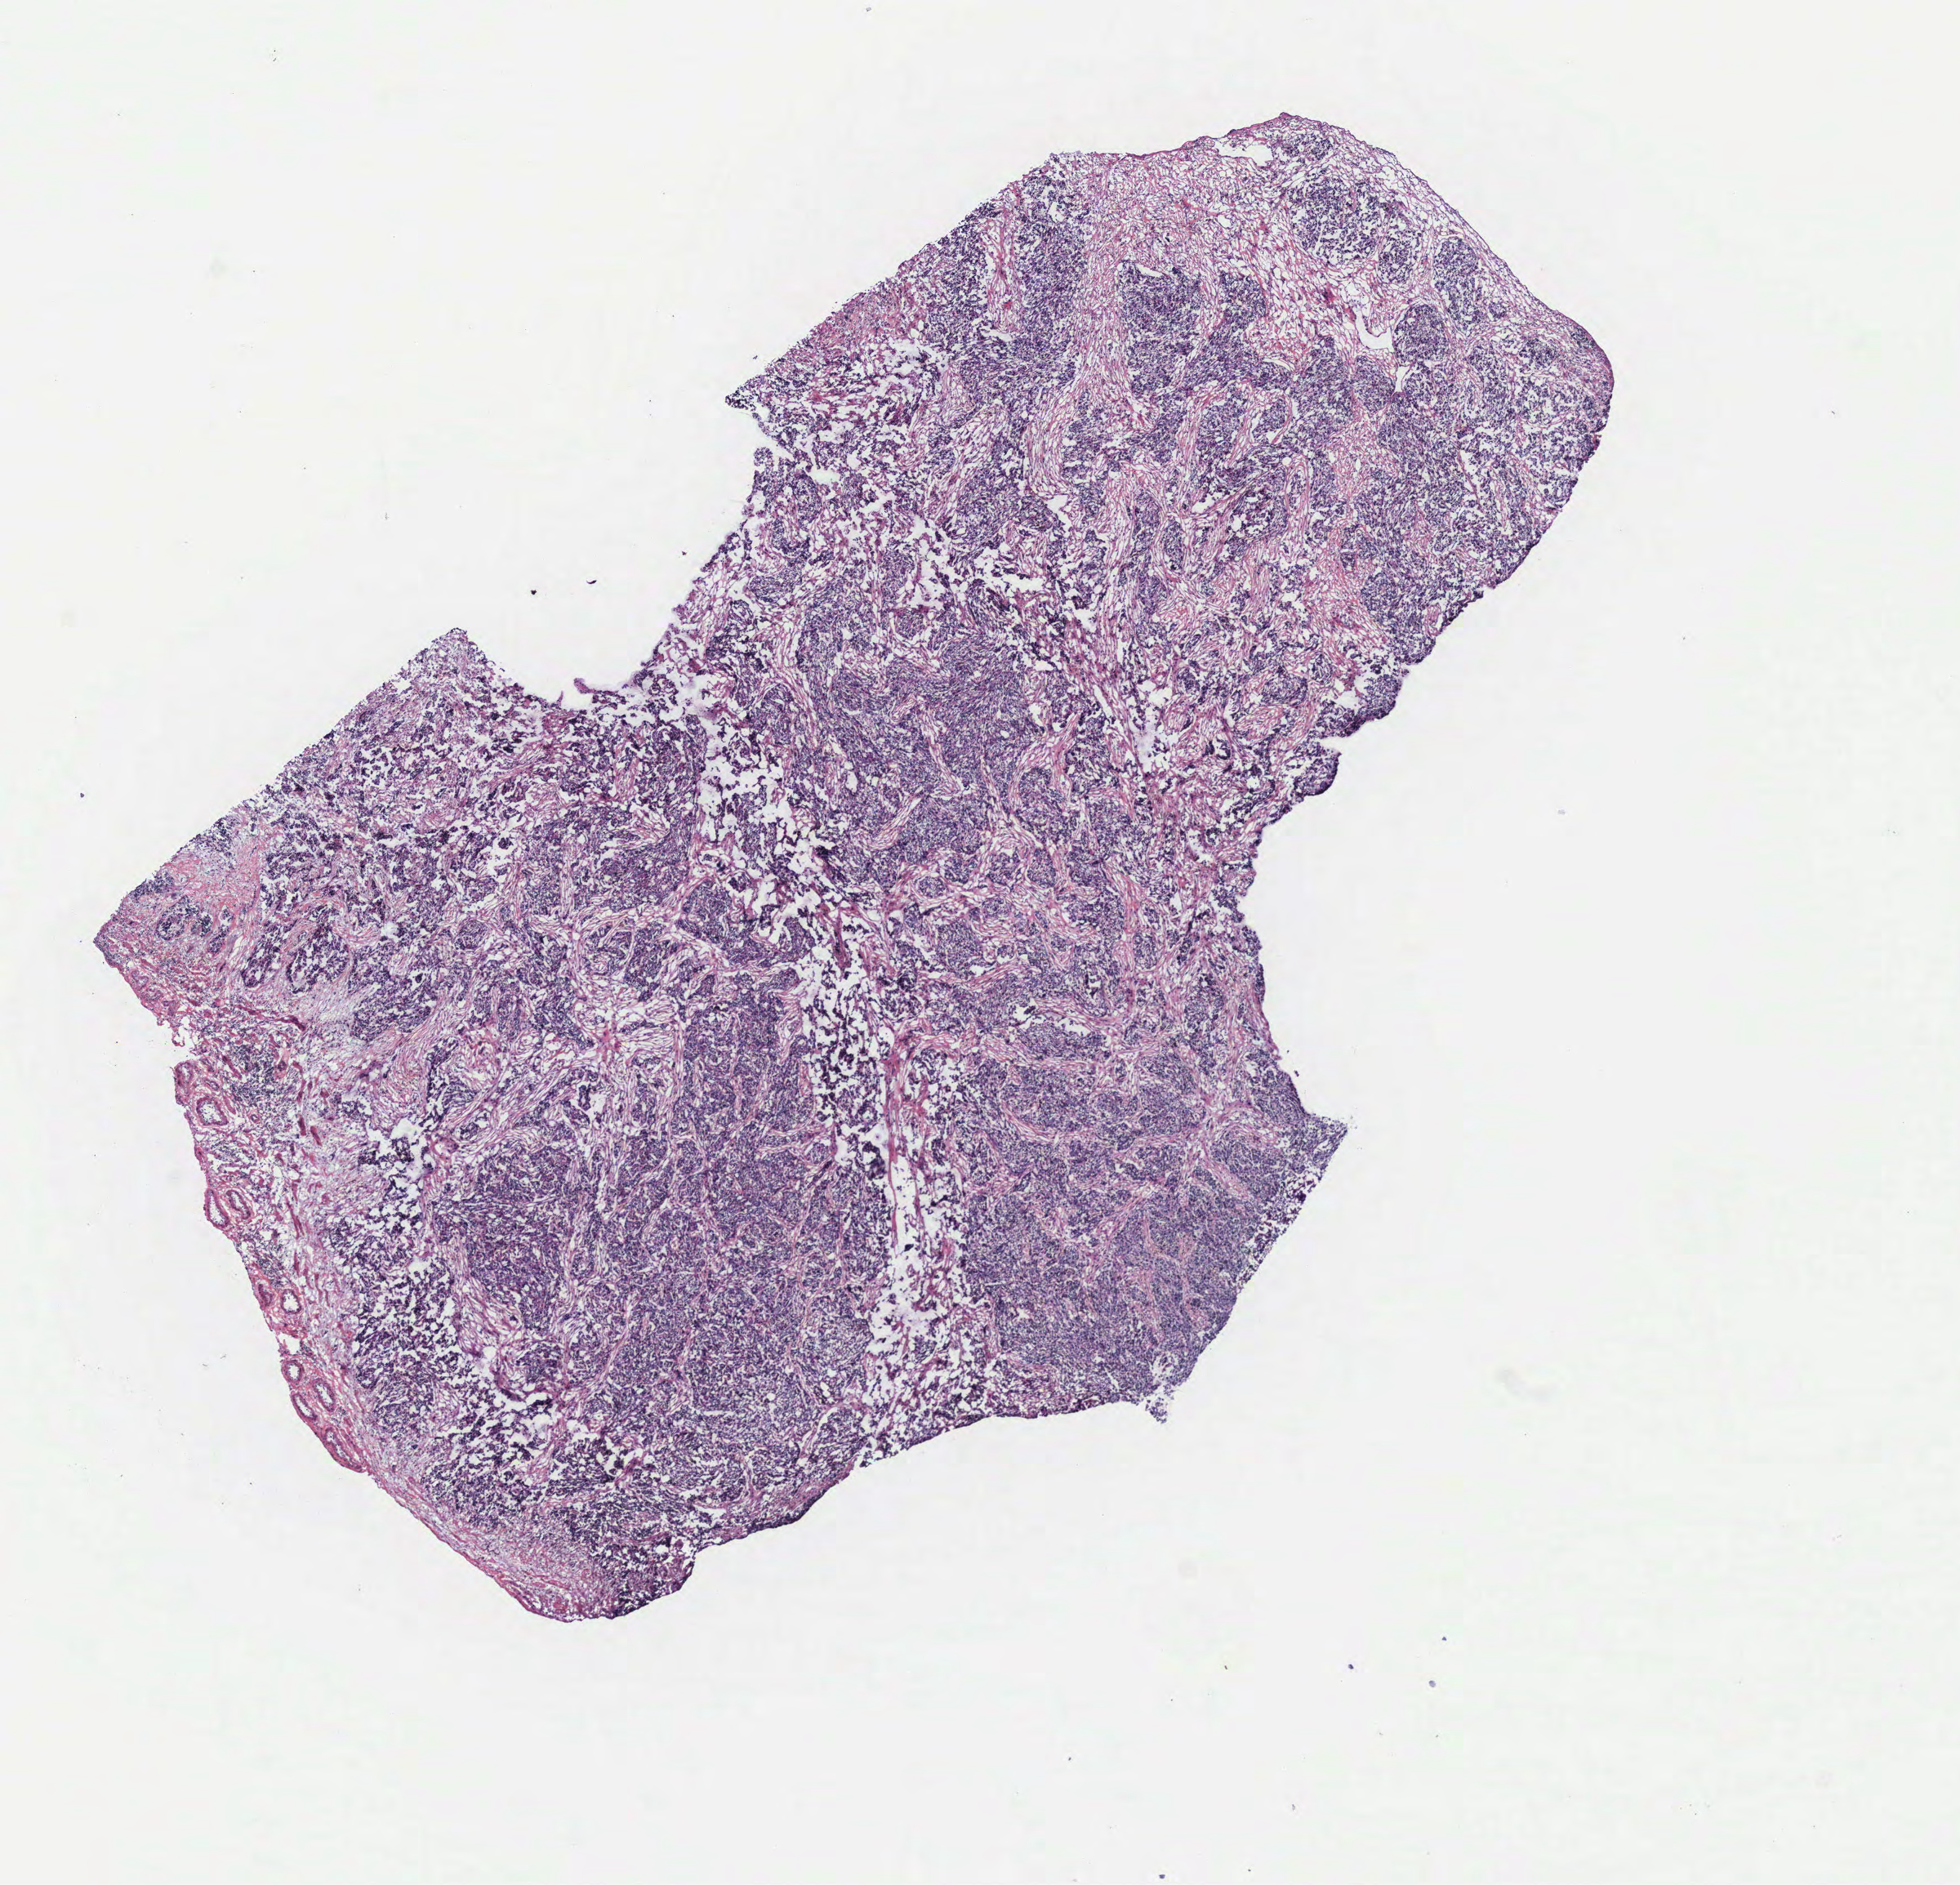
H&E whole-slide image — whole scanned area (about 9.6 x 9.2 mm) shown as a low-resolution overview. Tumour tissue sample, ovary. Female, 77 y/o.
- histologic diagnosis: Serous adenocarcinoma, NOS
- primary tumour site (as recorded): ovary